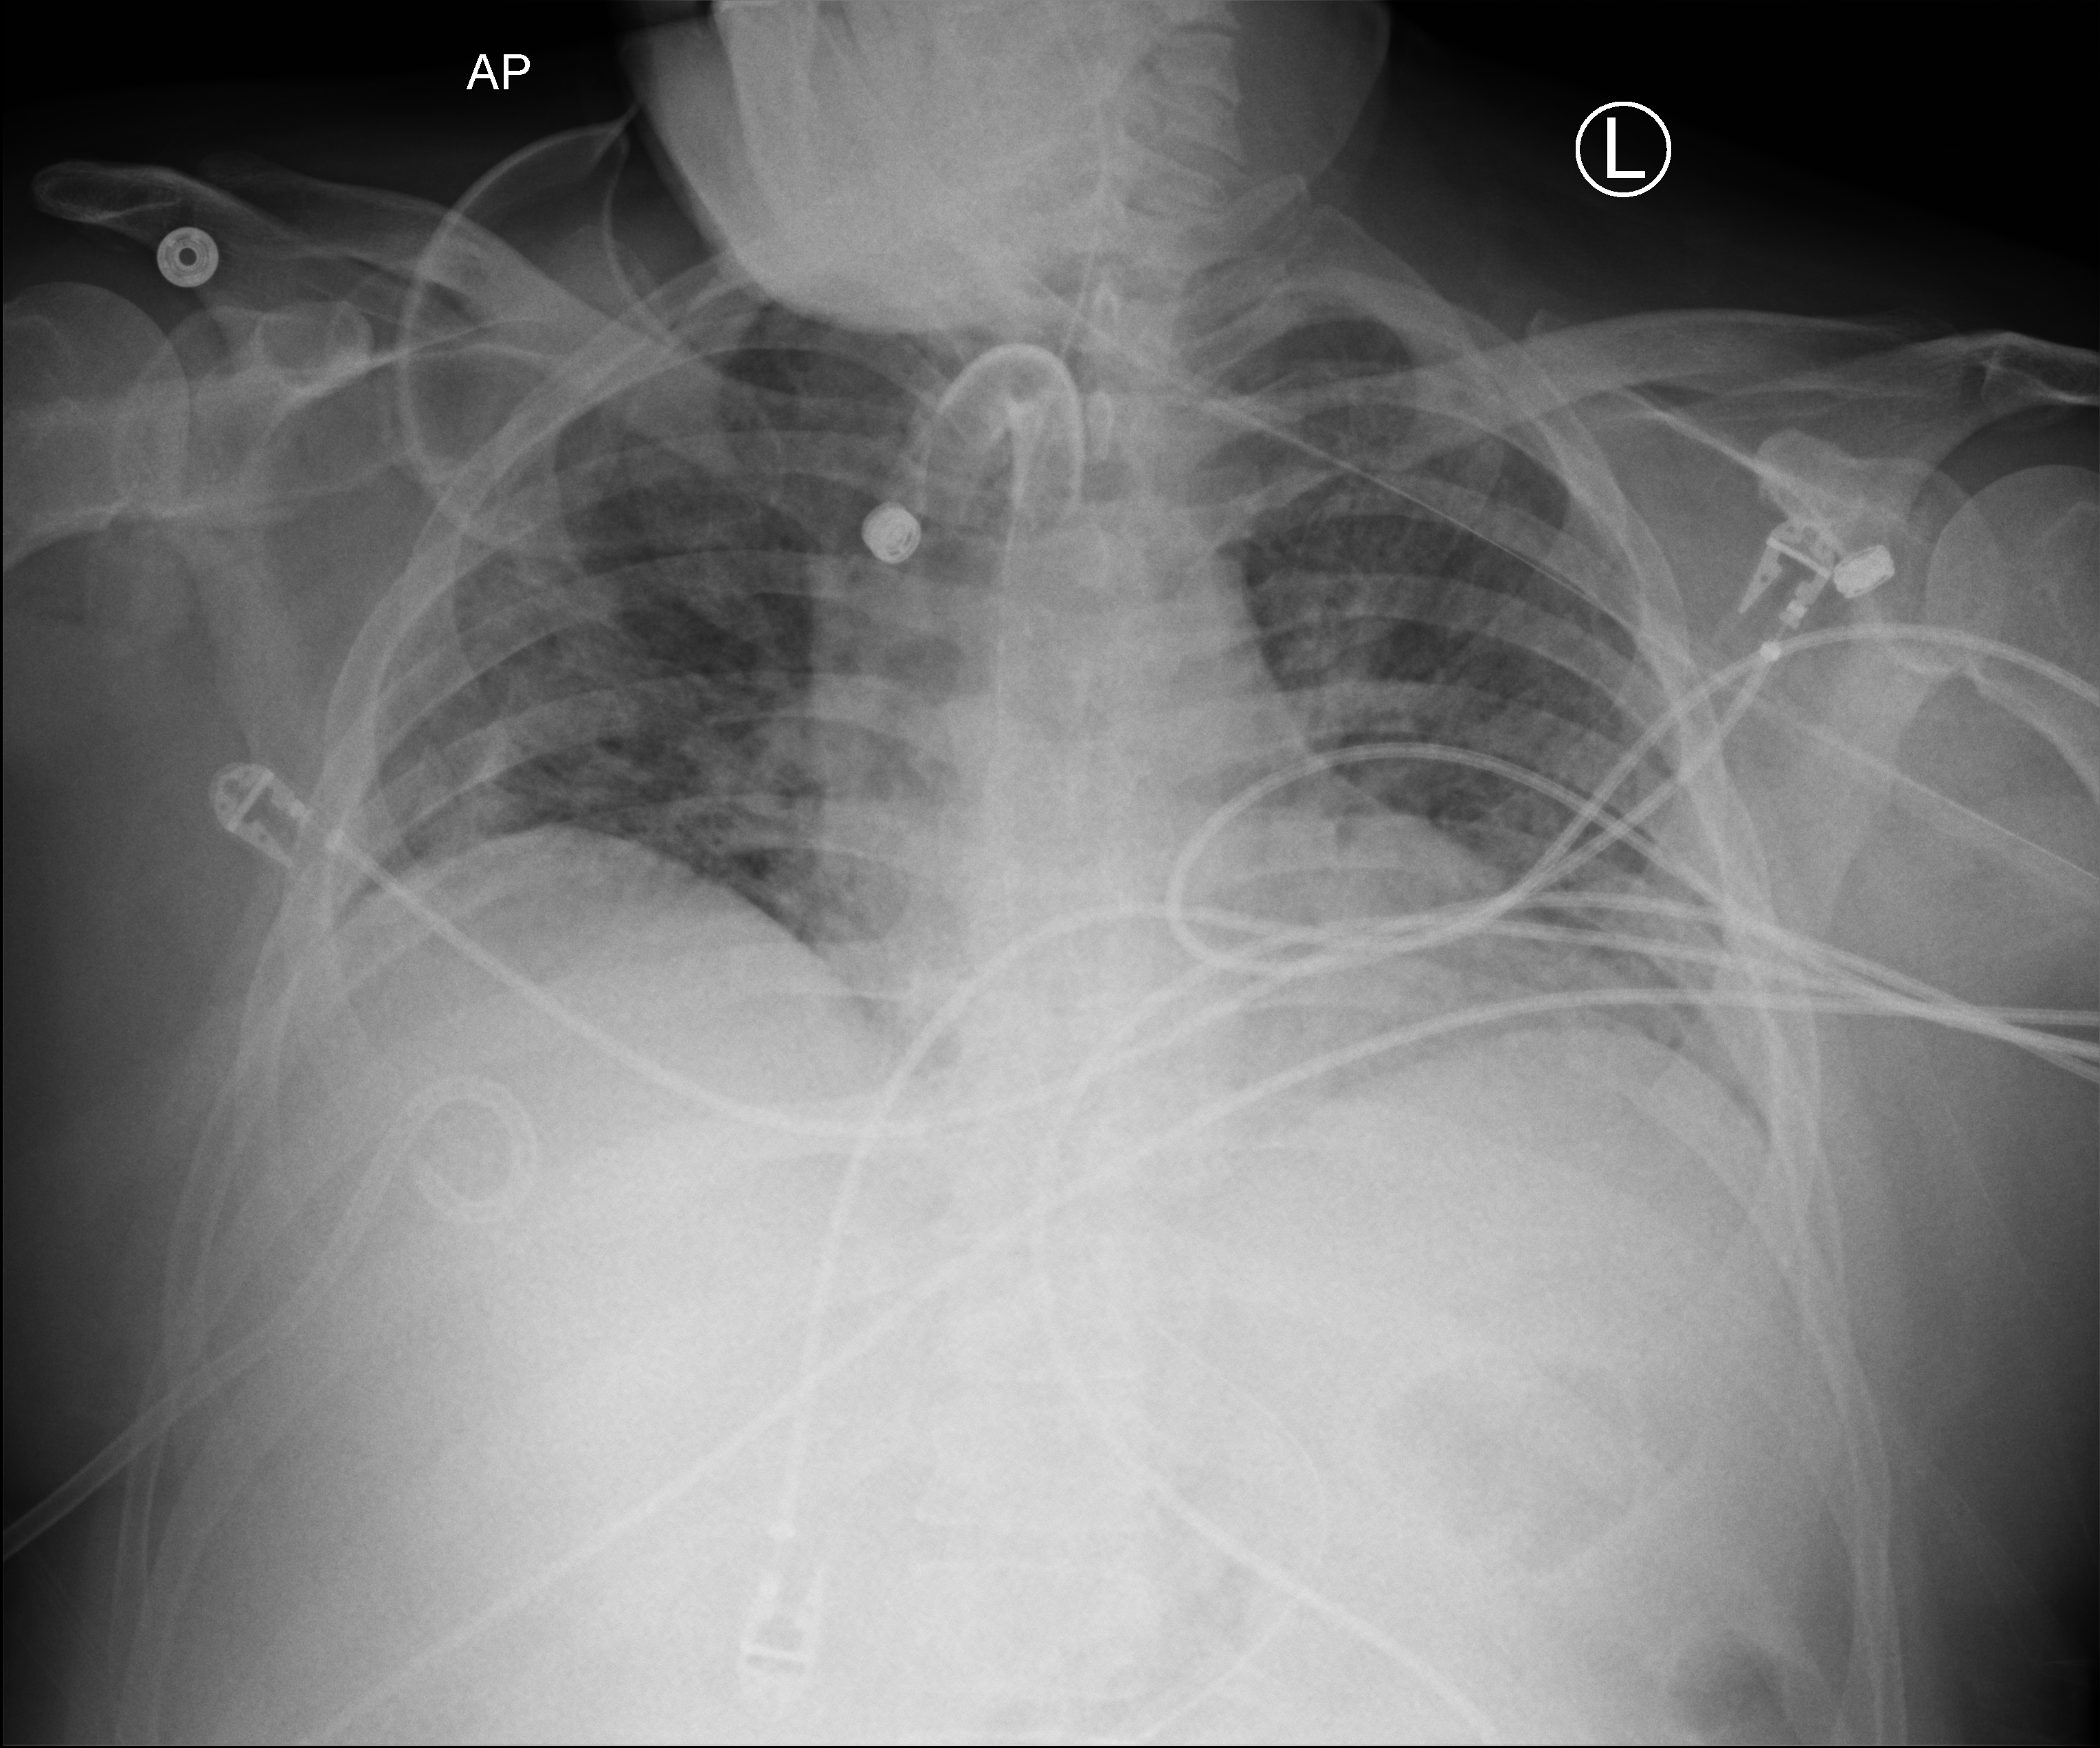
Bedside chest radiograph (computed radiography); anteroposterior (AP) projection. Male patient hospitalised with COVID-19, age 18–59 years.
Admission-level facts for this patient (not findings on this image; timing relative to this image not recorded): mechanically ventilated during this hospital stay: yes; other chronic lung disease (admission record): no; chronic kidney disease (admission record): no.